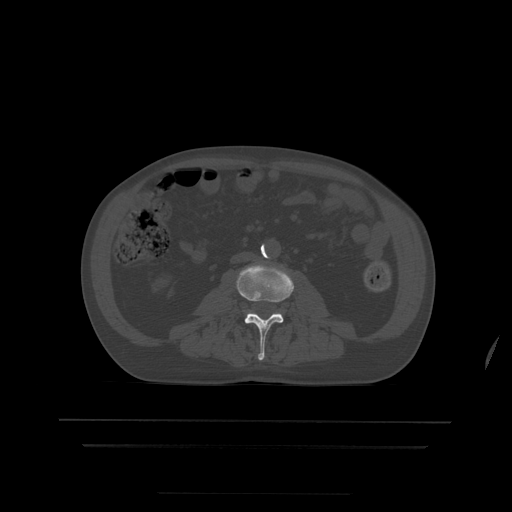
CT including the spine, one axial slice; position 115 of 522 along the scan axis; bone window (W 1800 / L 400 HU); 1.25 mm slice thickness; 512 × 512 image matrix, field of view 436 × 436 mm. Patient age 68 years. Case-level facts recorded for this patient, not image findings: primary cancer: urothelial.
Annotated regions visible in this slice (semi-automatically segmented with operator editing):
- L3 vertebra: bounding box (x1, y1, x2, y2) in pixels: (237, 264, 294, 361)